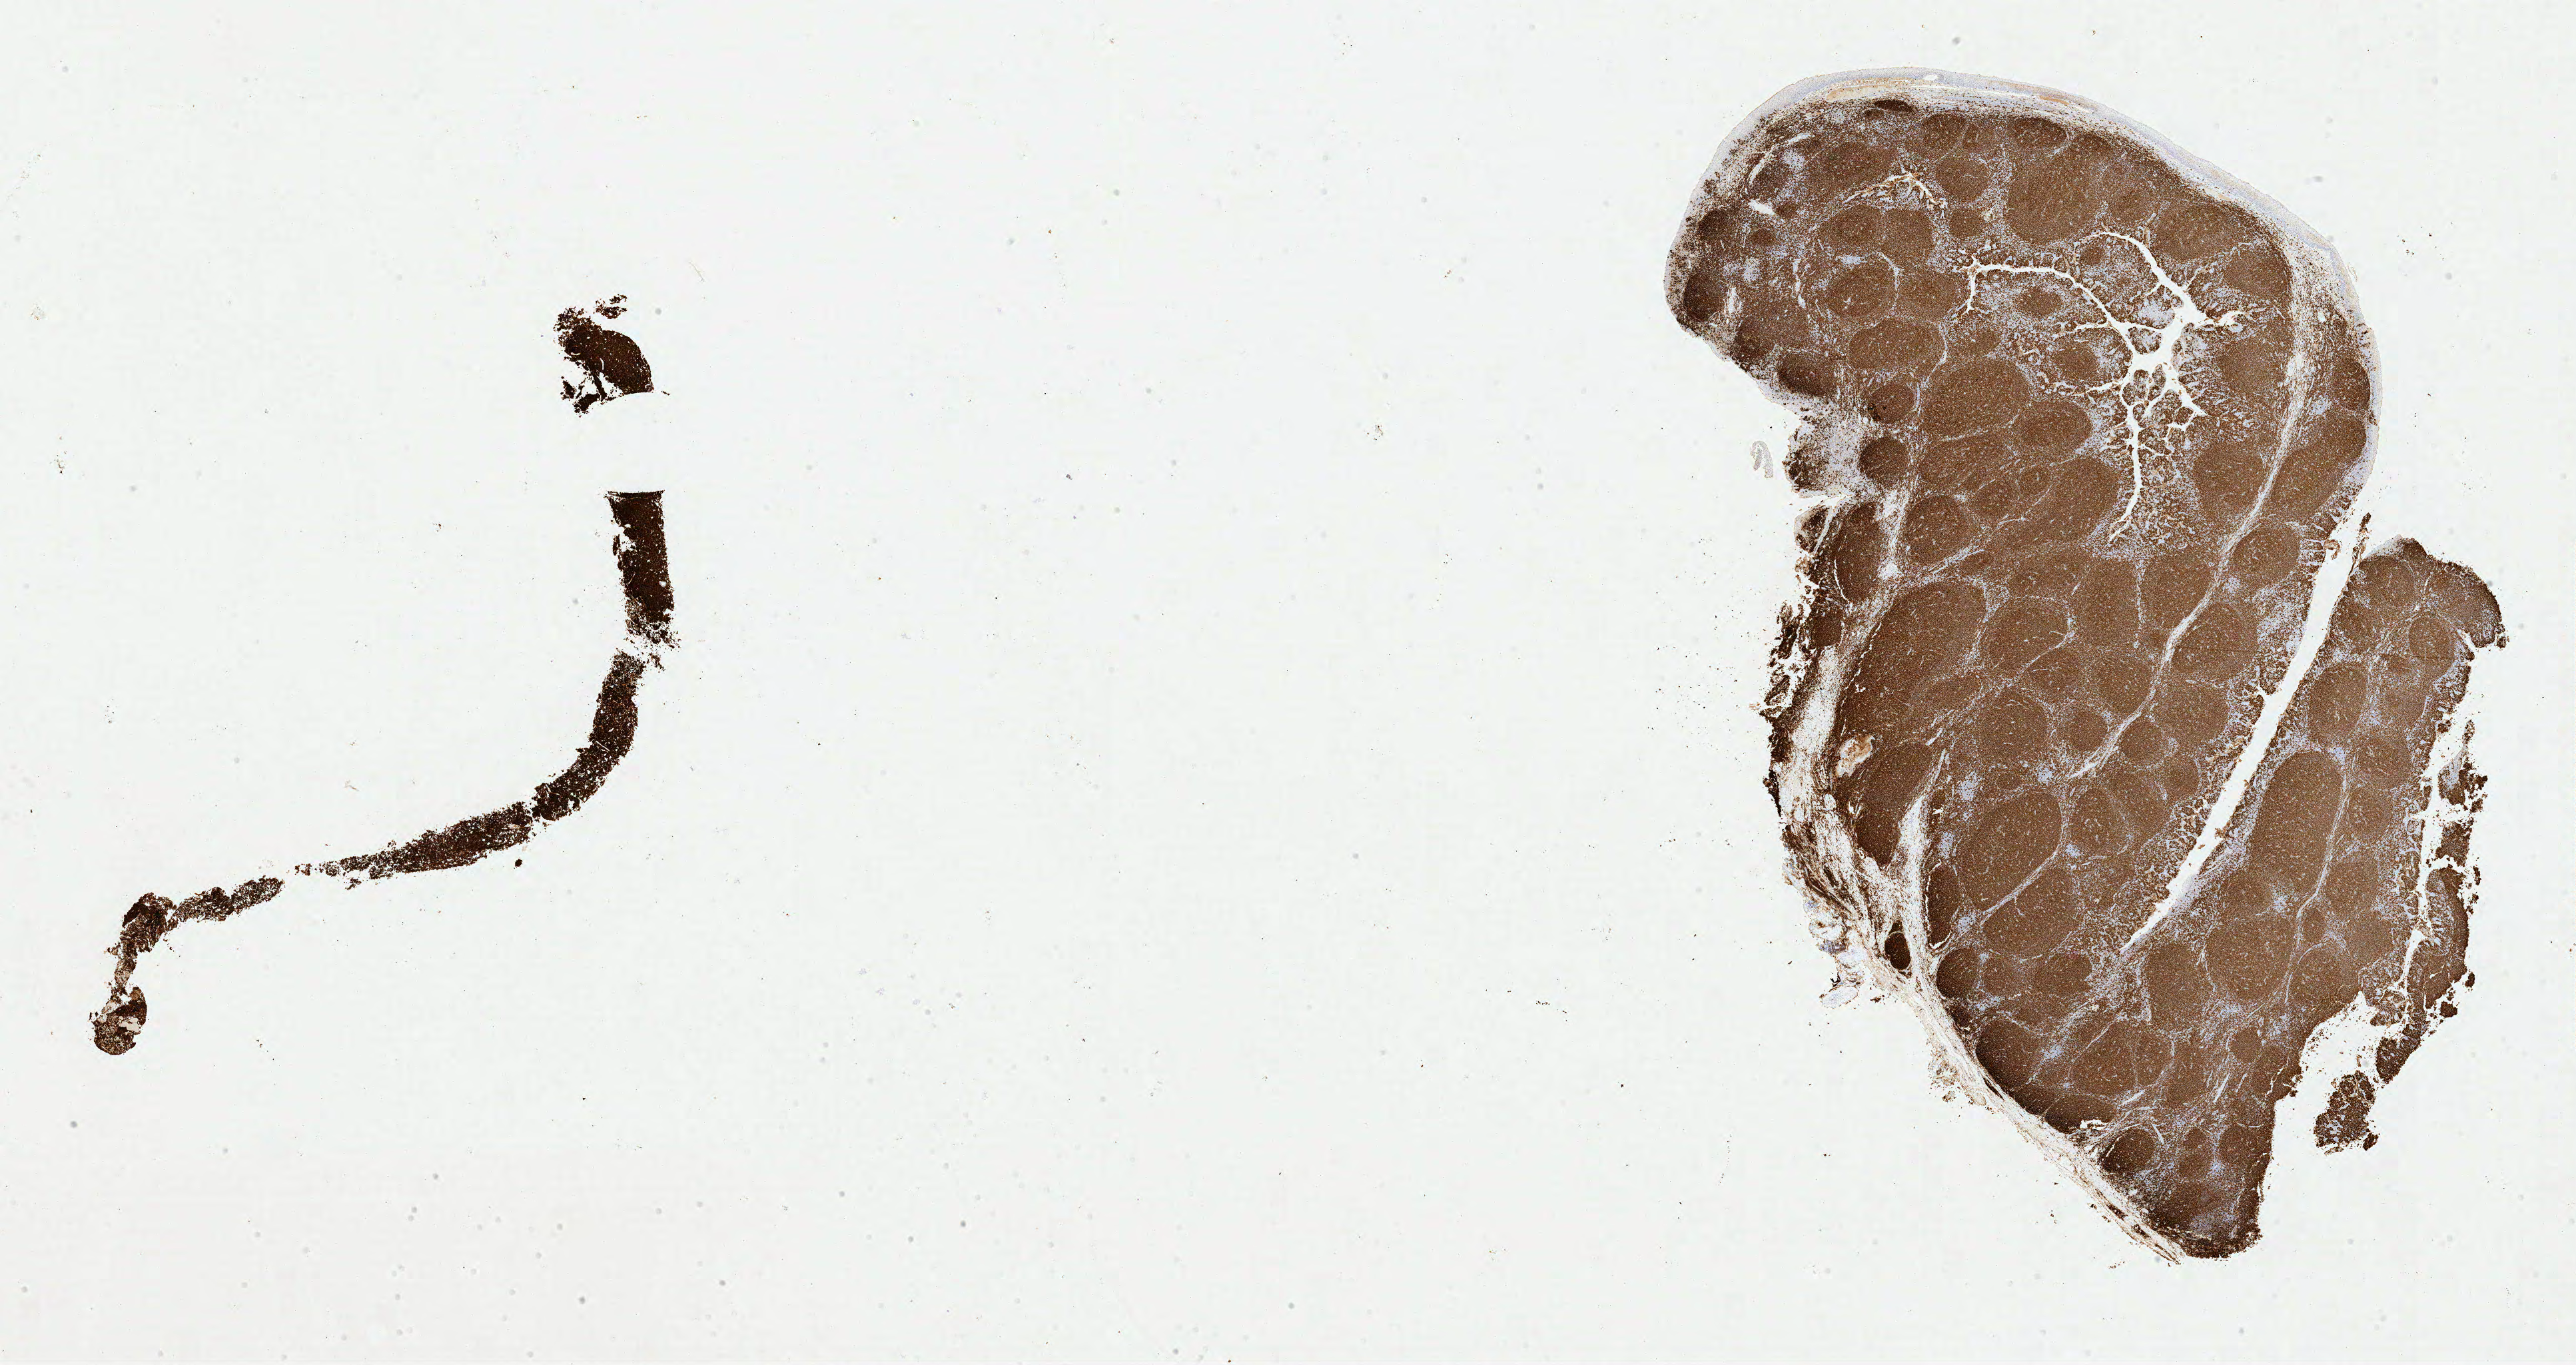
IHC for CD20, whole-slide image, low-resolution overview of the scanned area, about 30.5 x 16.2 mm, tumor tissue, site: ovary. Female, age 7 years at initial diagnosis.
Histologic diagnosis: Burkitt lymphoma, NOS.